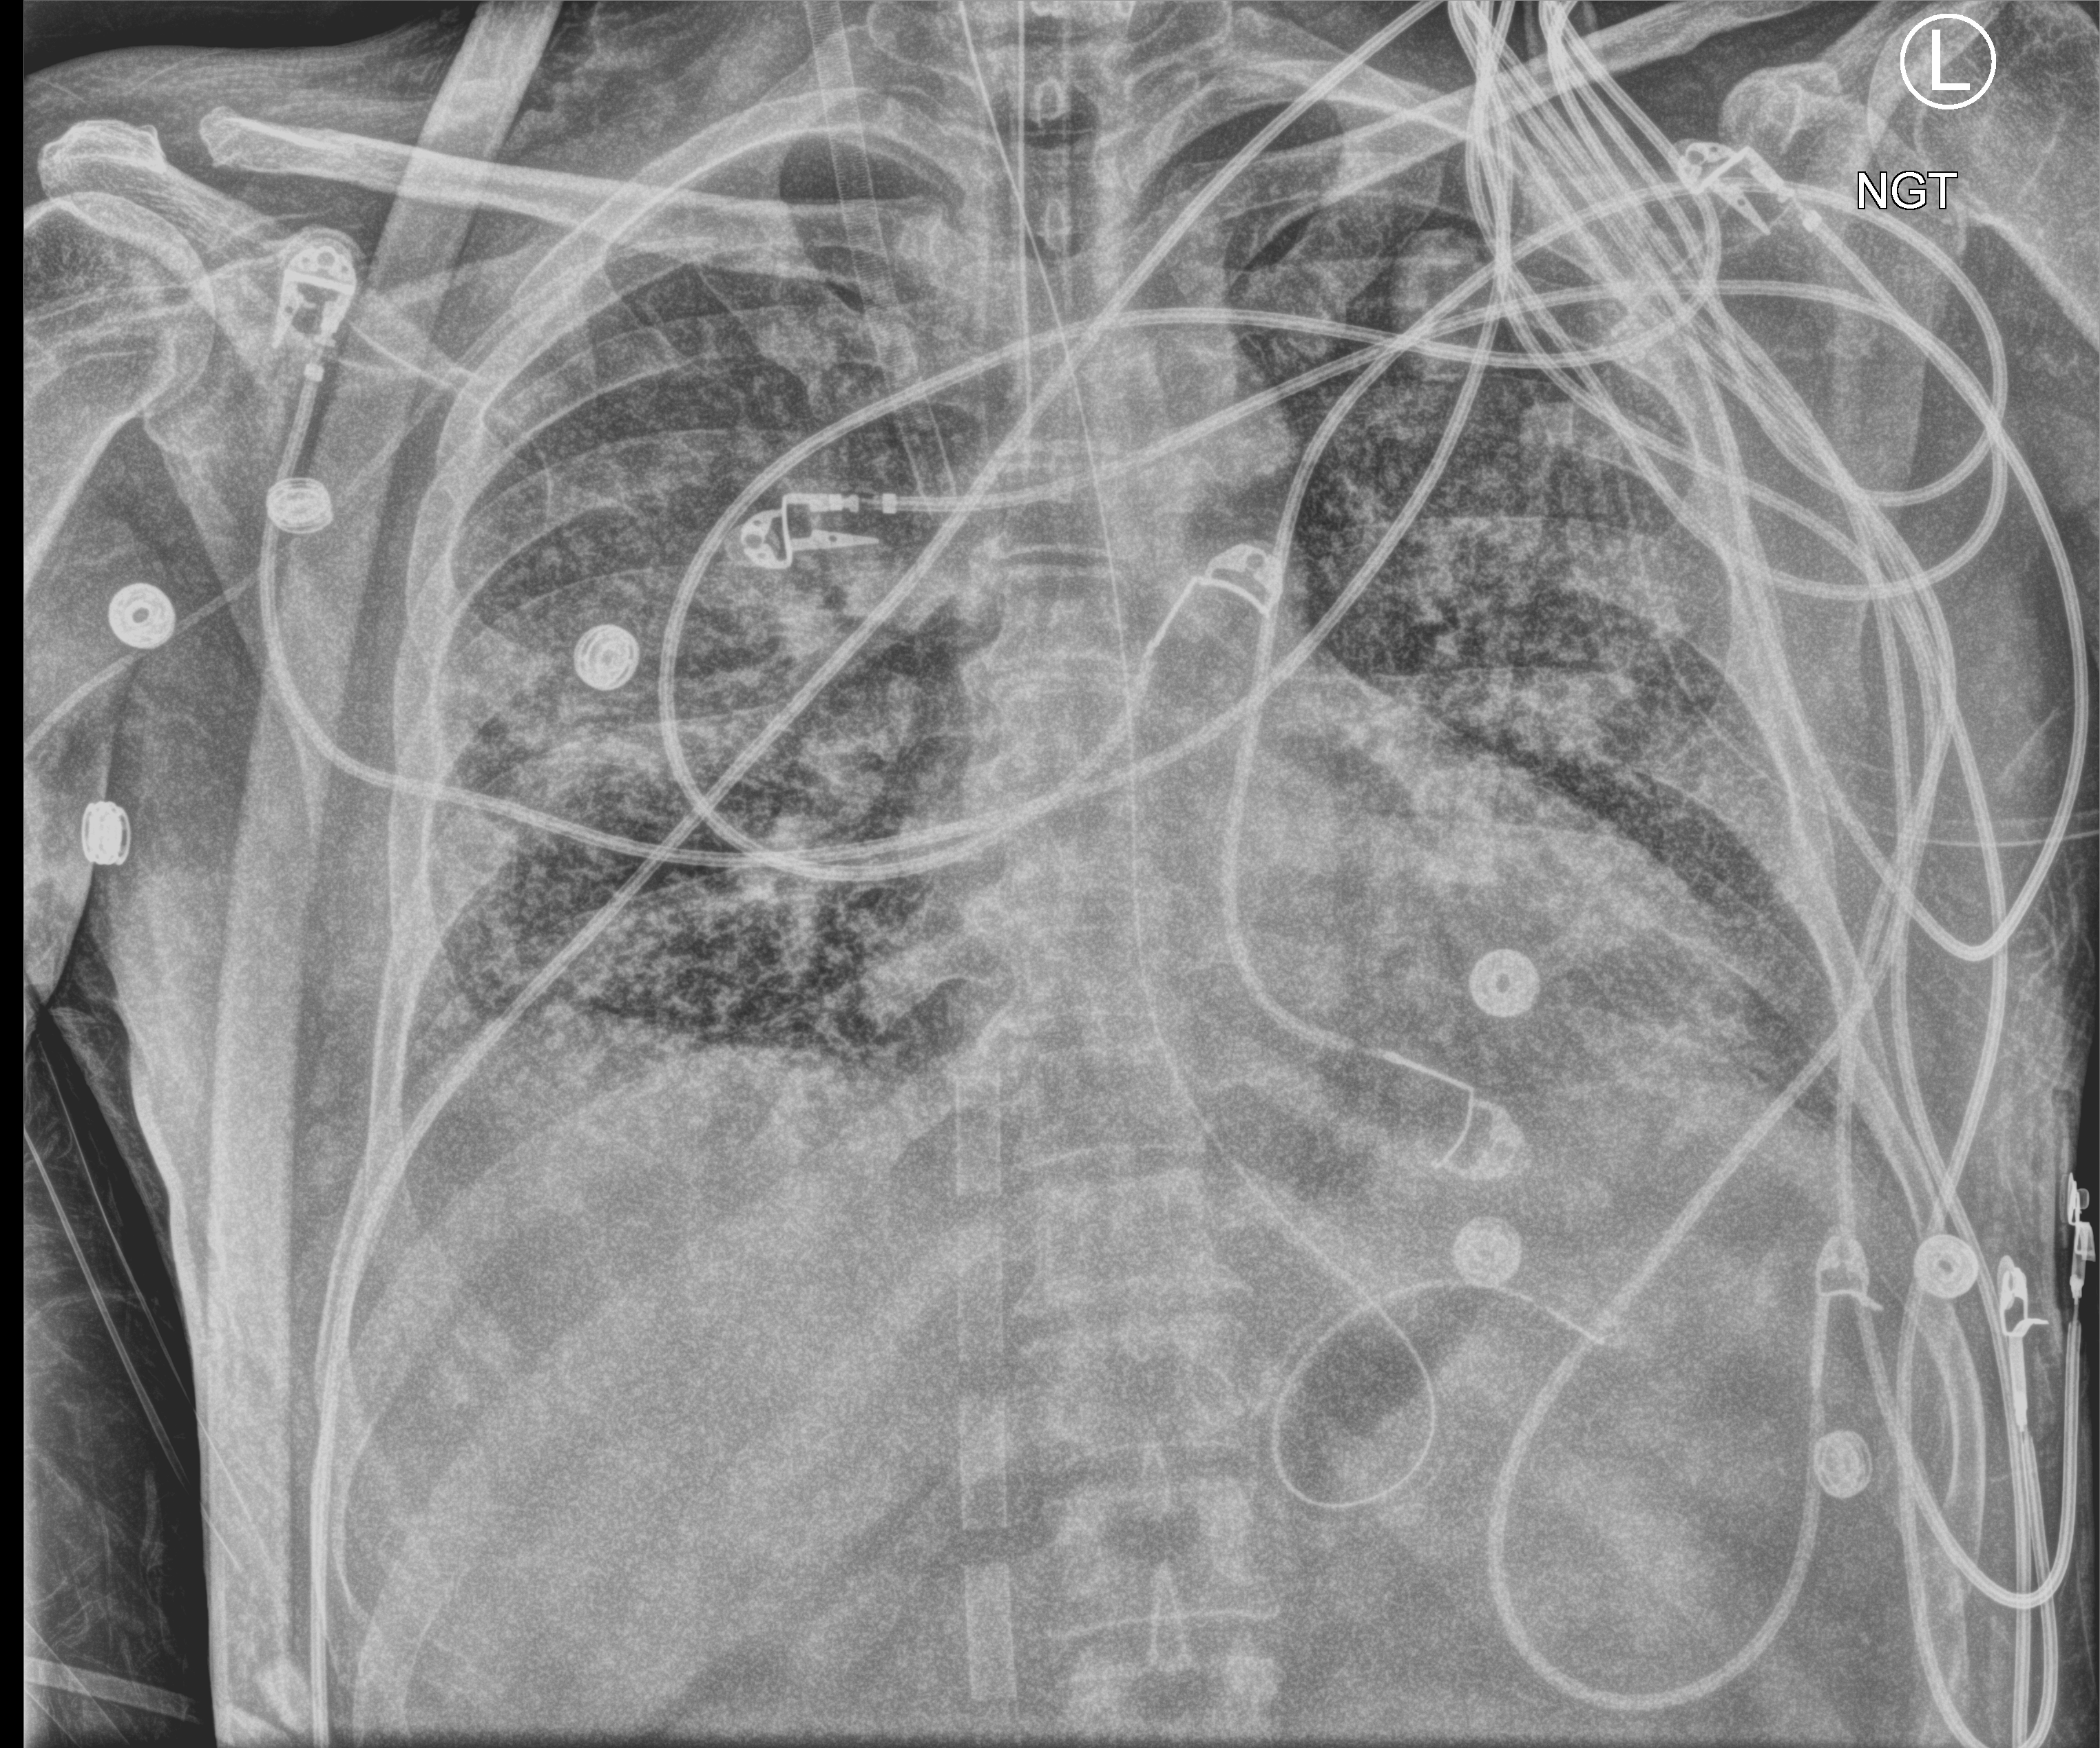
Bedside chest radiograph (computed radiography); anteroposterior (AP) projection. Patient hospitalised with COVID-19; male, aged 18–59 years.
Admission-level facts for this patient (not findings on this image; timing relative to this image not recorded): admitted to intensive care during this hospital stay: yes; diabetes (admission record): no.